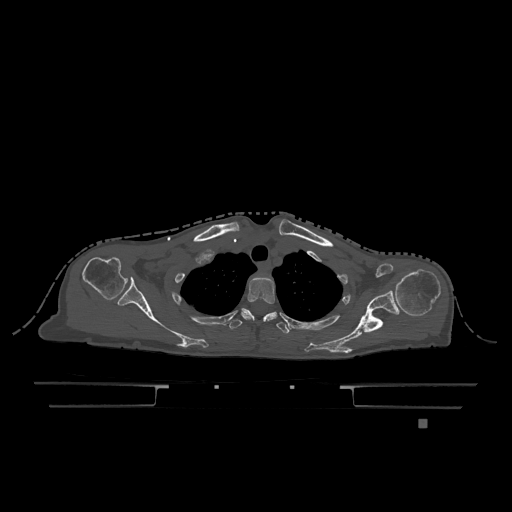
CT including the spine, one axial slice; slice 950 of 1317 in the series (ordered by position); bone window (W 1800 / L 400 HU); 0.5 mm slice thickness; 512 × 512 image matrix. Female patient, age 74 years. Case-level facts recorded for this patient, not image findings: primary cancer: lung.
Outlined on this slice (semi-automatic segmentation, software-assisted and operator-edited):
- T2 vertebra: bounding box [x1, y1, x2, y2] px = [241, 276, 277, 321]
- T3 vertebra: [229, 309, 290, 334]
- T6 vertebra: [251, 312, 277, 320]